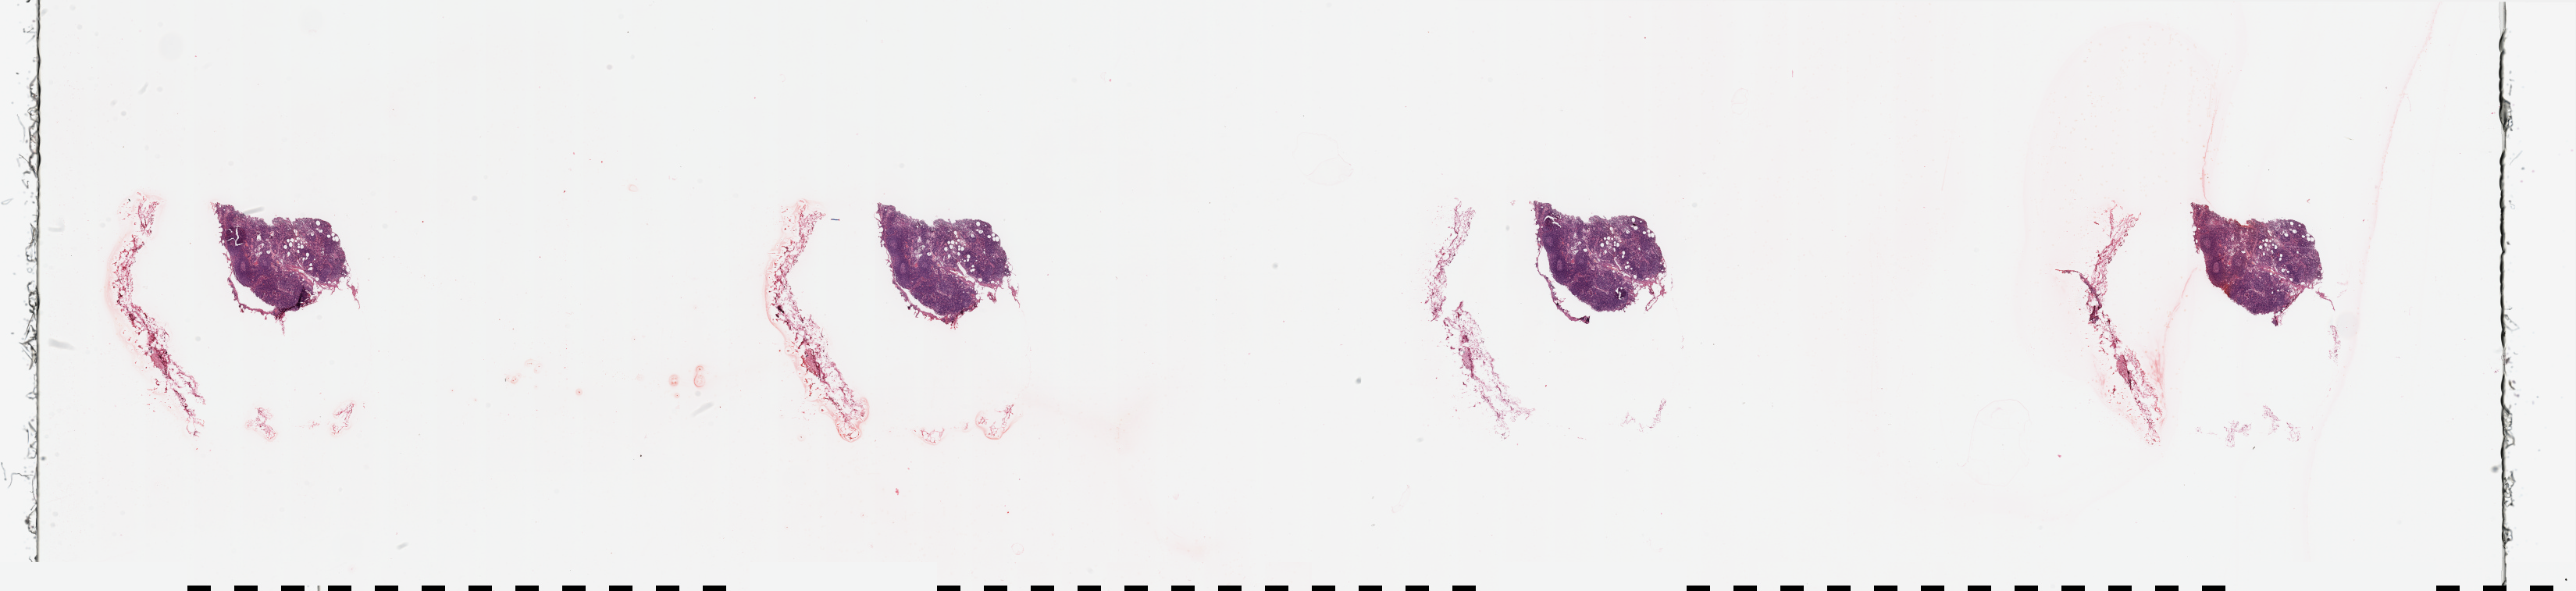
H&E whole-slide image, shown as a low-resolution overview of the whole scanned area (about 52.2 x 12.0 mm); pancreas, normal (non-tumour) tissue. Male, 72 y/o.
This section: normal (non-tumour) tissue from the same patient. Patient diagnosis: Infiltrating duct carcinoma, NOS.